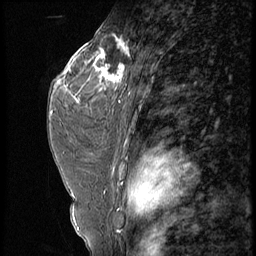
Breast MRI (dynamic contrast-enhanced), one sagittal slice; slice 35 of 56 in the series (ordered by position); 4 images stored at this slice position (order not interpretable as contrast timing); 1.5 T; TE 4.2 ms, TR 9 ms; 2.5 mm slice thickness; 256 × 256 image matrix. Patient: female, 44 years. Case-level facts recorded for this patient, not image findings: setting: breast cancer imaged before/during neoadjuvant chemotherapy; receptor status: triple-negative.
Annotated regions visible in this slice (semi-automatic segmentation, software-assisted and operator-edited):
- analysis volume of interest (the breast-tissue region the enhancement analysis was run in; not a lesion): box from (x=87, y=28) to (x=132, y=99) px
- tumour enhancement mask (voxels above the 140 % enhancement threshold inside the analysis volume of interest): (x=87, y=35)–(x=130, y=84)